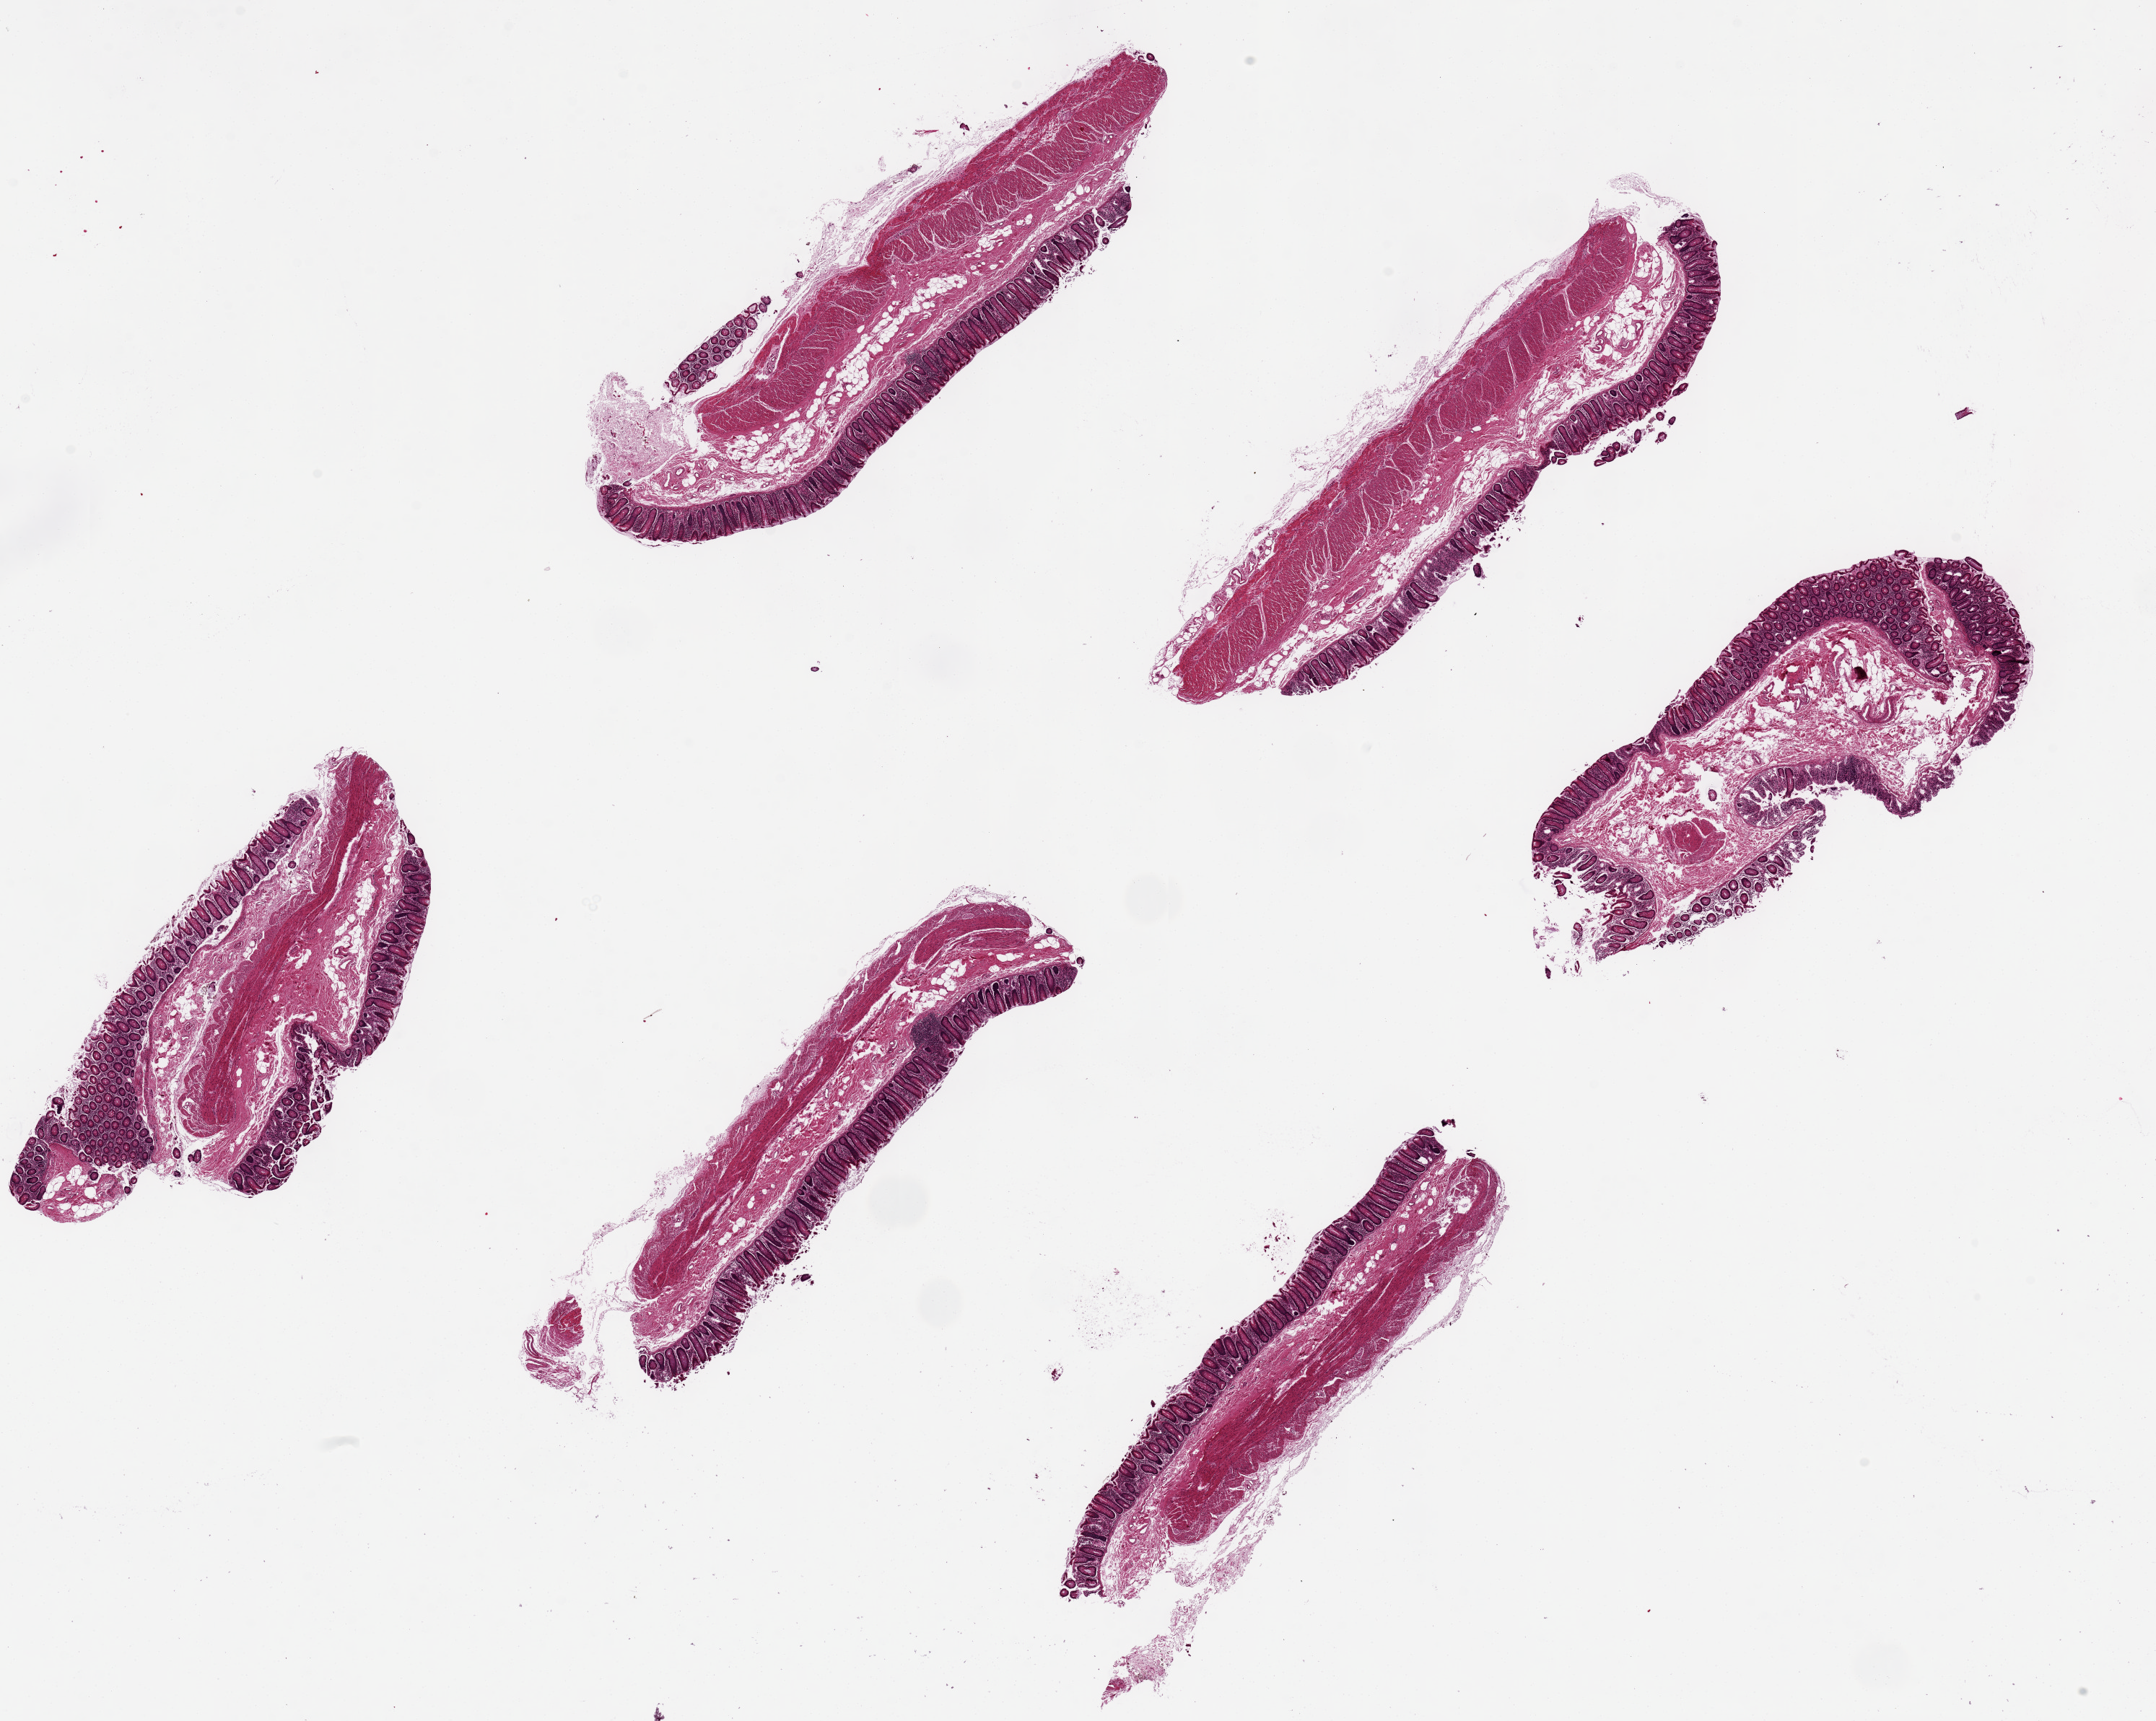
Digitized H&E-stained section, brightfield — a low-resolution overview of the entire scanned area, about 23.6 x 18.9 mm; PAXgene-fixed paraffin-embedded (PFPE) section; target tissue: transverse colon; tissue donor sample. Donor: male.
Review note (as recorded): 6 pieces, mucosa less well preserved, 15-20% of thickness.